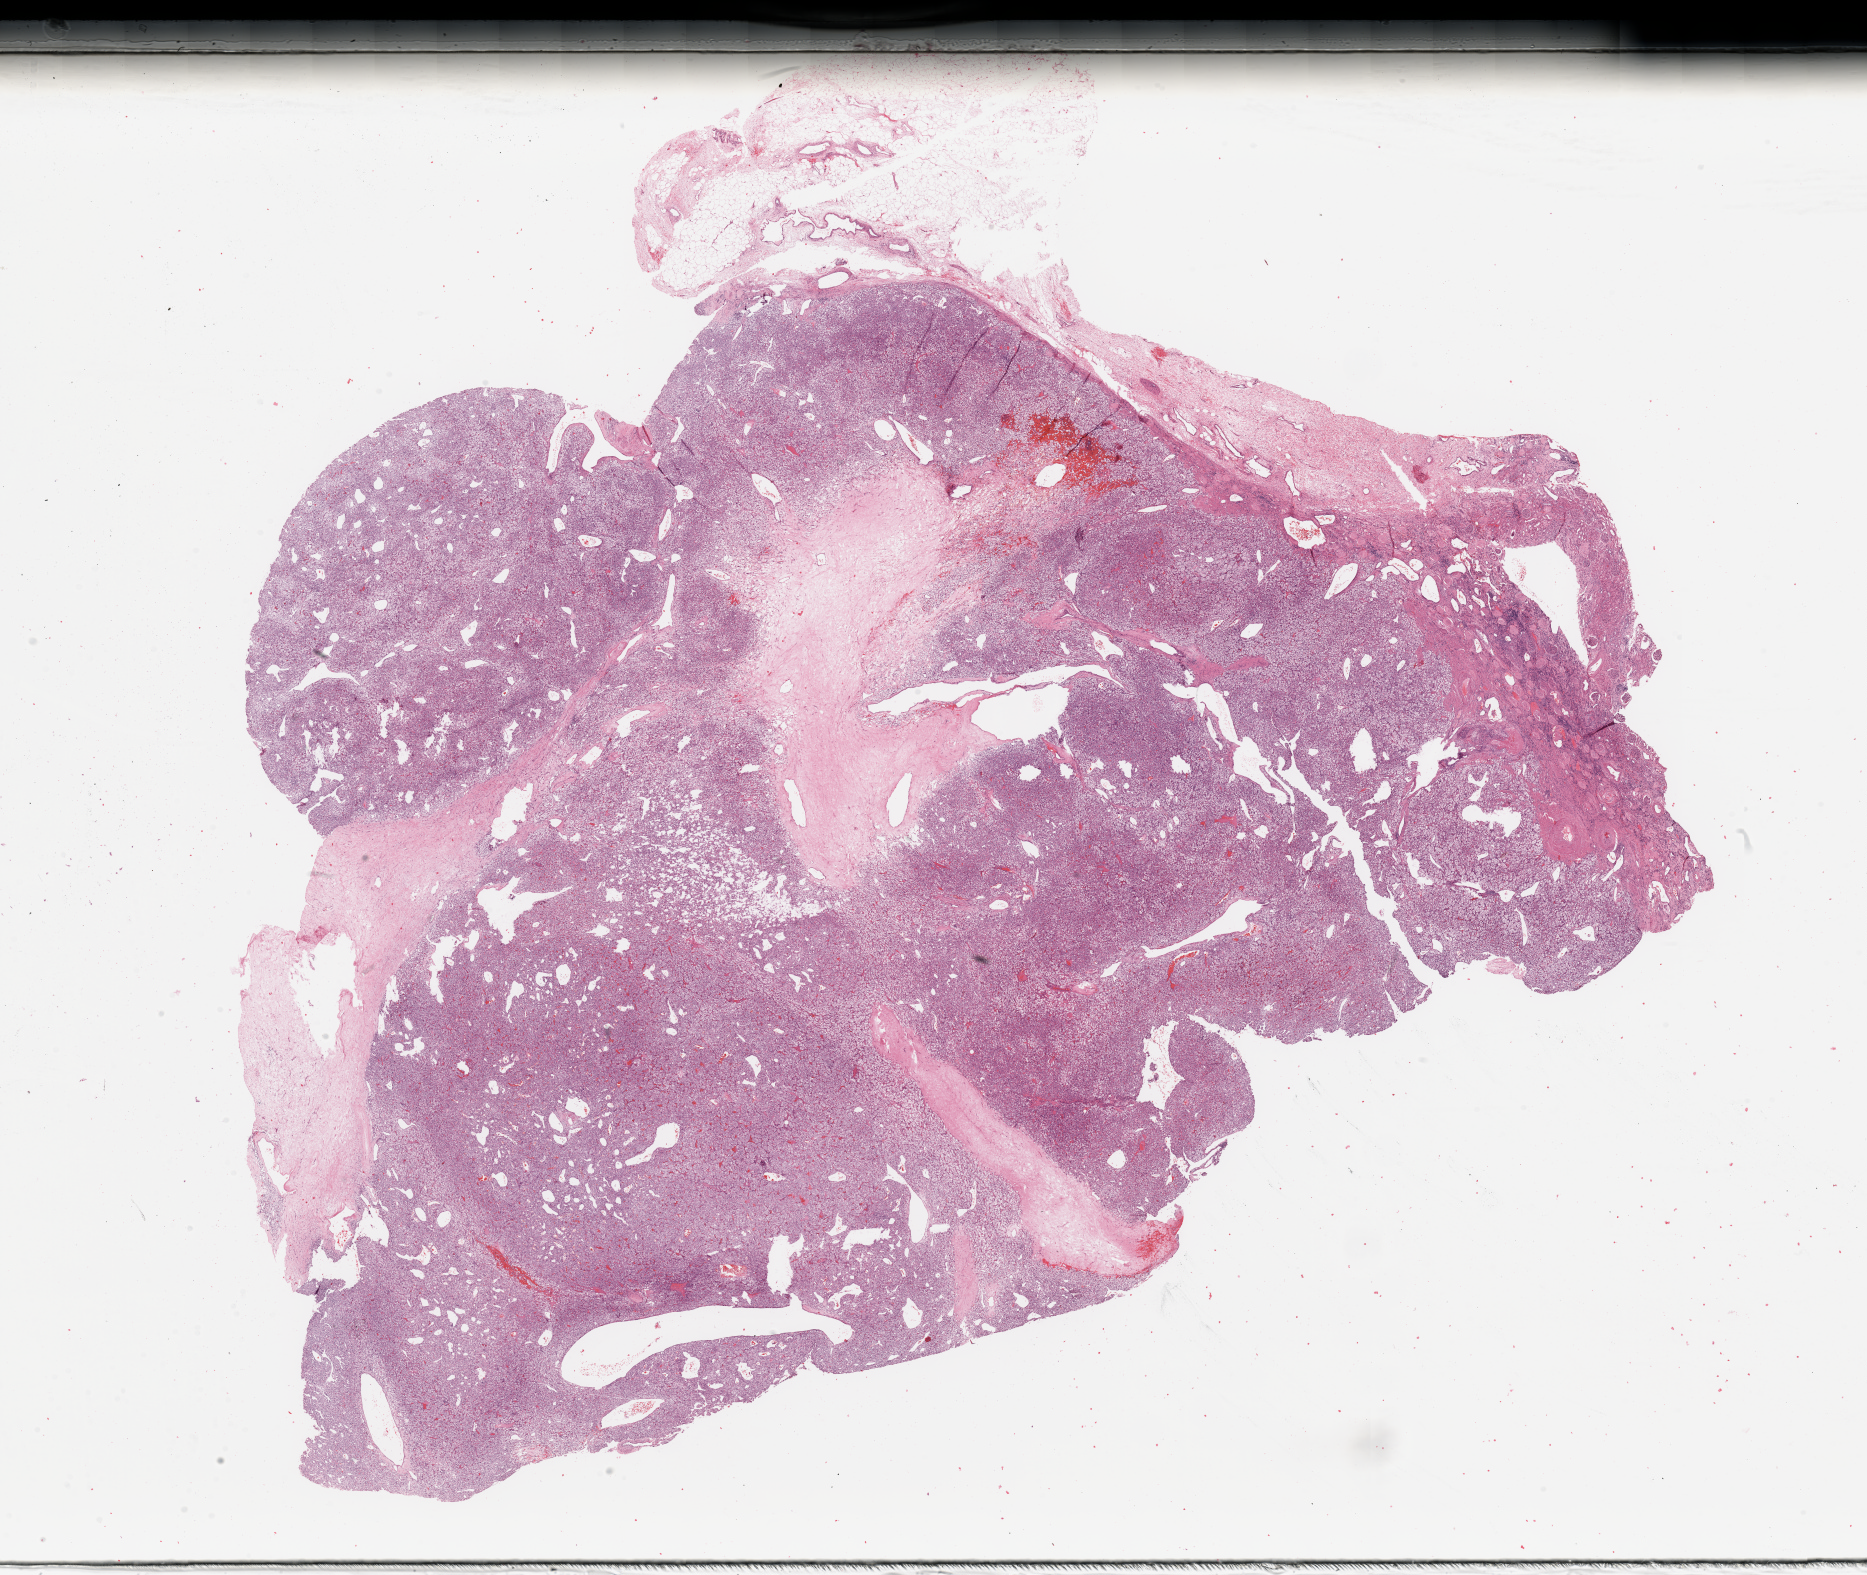
Whole-slide histology image, Hematoxylin and eosin (H&E) stained — low-resolution overview of the scanned area, about 29.5 x 24.9 mm (slide scanned at 20x). Kidney, tumour tissue. 76-year-old female patient. Histologic grade: G2 (moderately differentiated).
Diagnosis: Renal cell carcinoma, NOS.